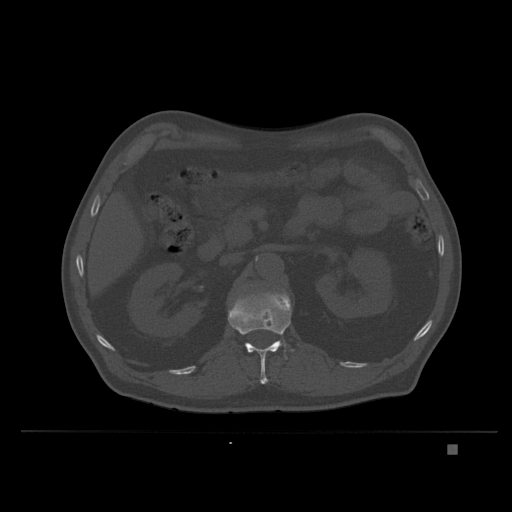
CT including the spine, one axial slice. Position 135 of 435 along the scan axis. Bone window (W 1800 / L 400 HU). 512 × 512 image matrix. Patient: male, 73 years. From the clinical record (not read from this slice): primary cancer: skin.
Outlined on this slice (semi-automatically segmented with operator editing):
- L1 vertebra: bounding box [x1, y1, x2, y2] px = [228, 289, 295, 384]